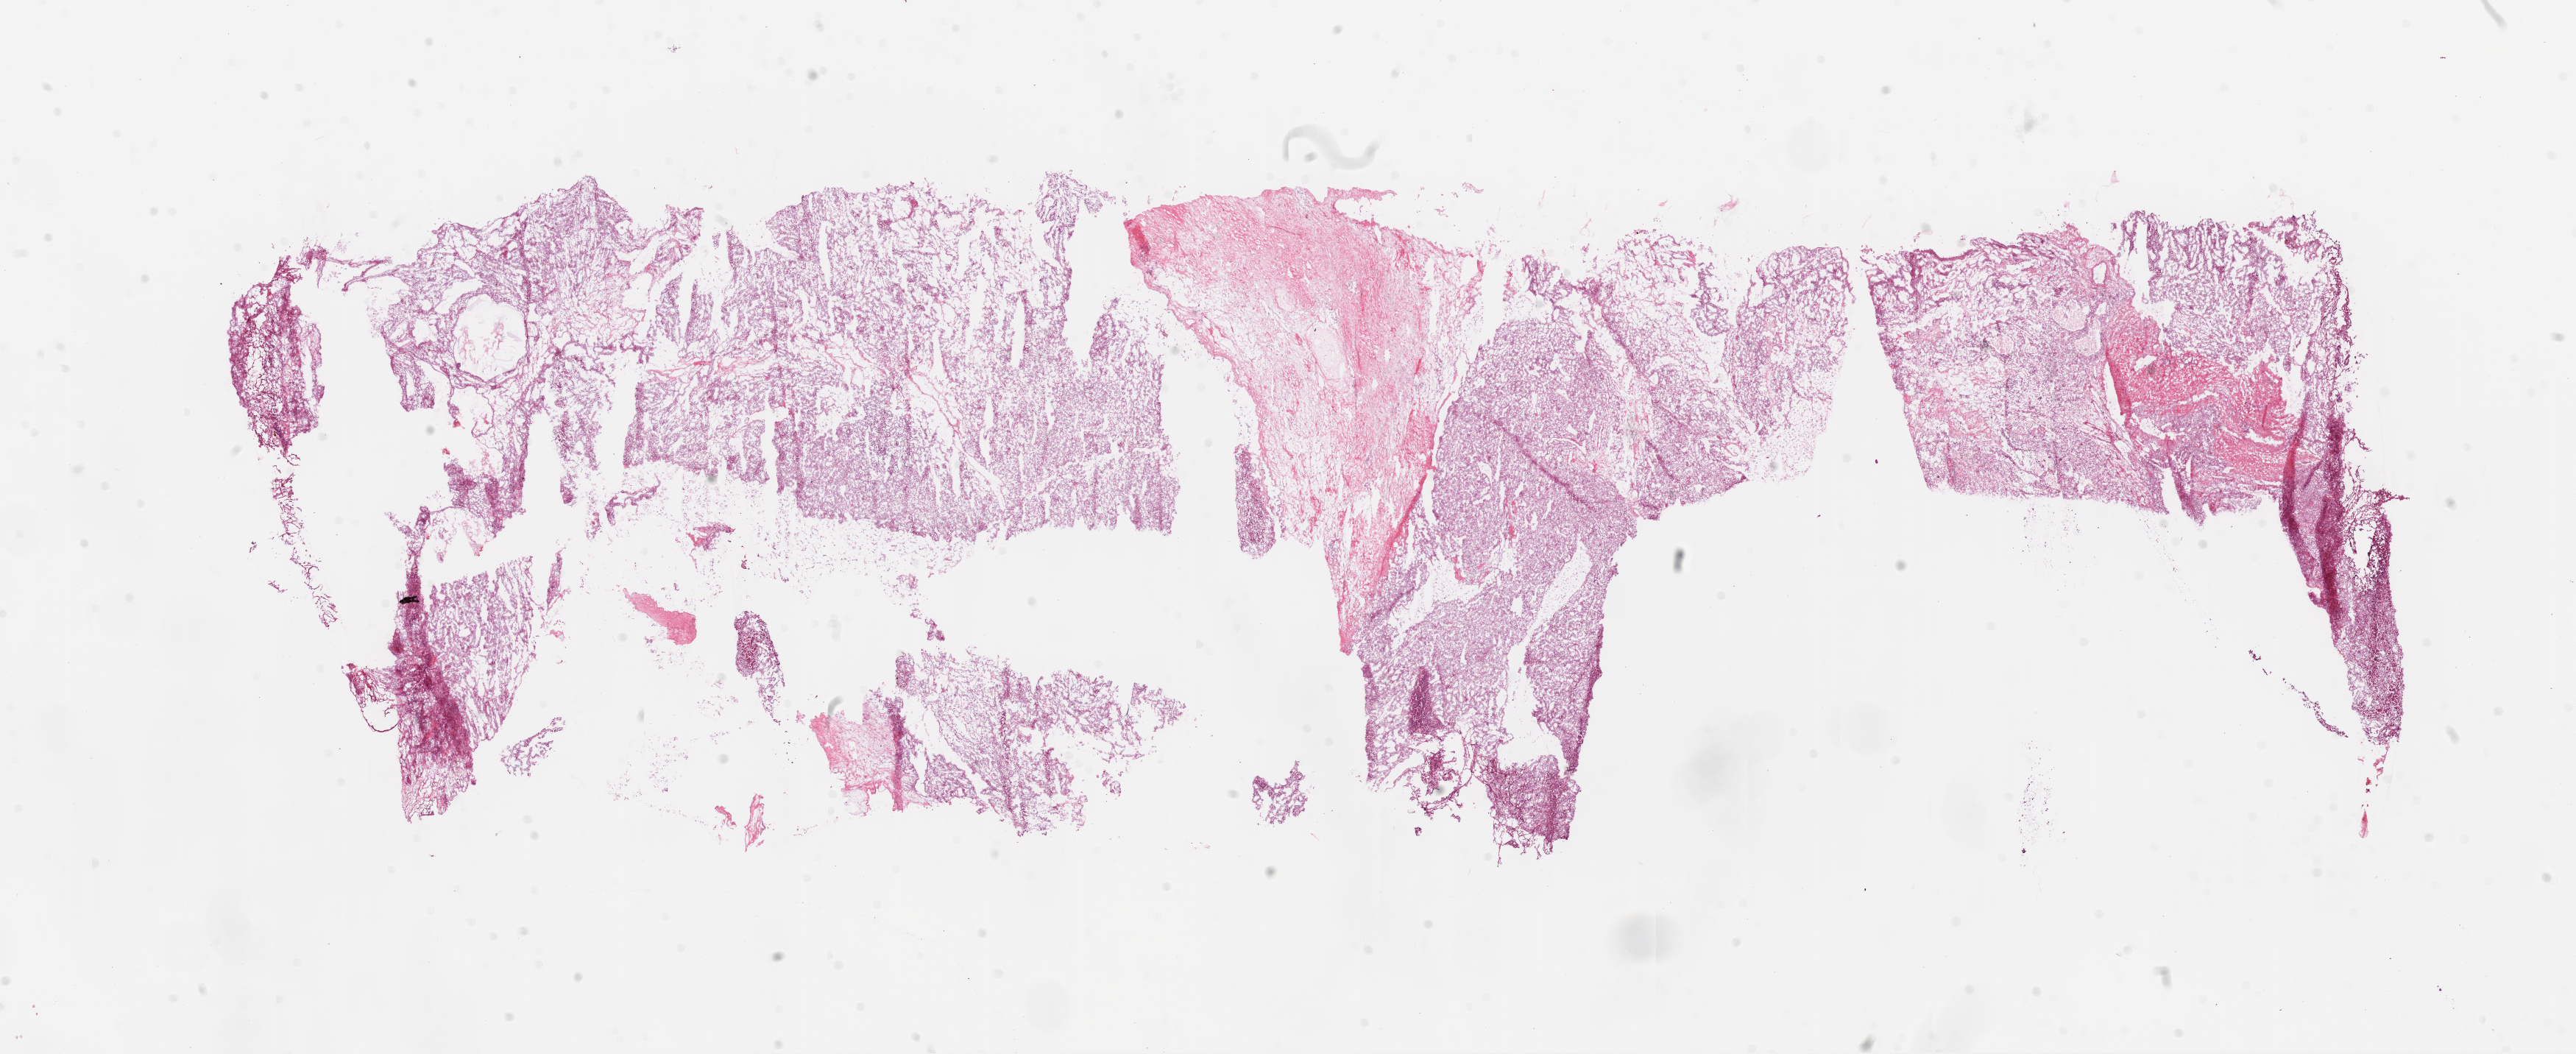
Digitized Hematoxylin and eosin (H&E) stained tissue section (whole slide) — shown as a low-resolution overview of the whole scanned area (about 28.1 x 11.5 mm). Frozen section. Kidney, primary tumour sample. Male patient; age at initial diagnosis 49 years. Histologic grade: G4 (undifferentiated). Pathologist review of this section (percent, as recorded): tumour cells 80%, tumour nuclei 80%, normal cells 0%, stromal cells 20%, necrosis 0%.
Diagnosis: Clear cell adenocarcinoma, NOS. AJCC pathologic stage: III (7th edition).